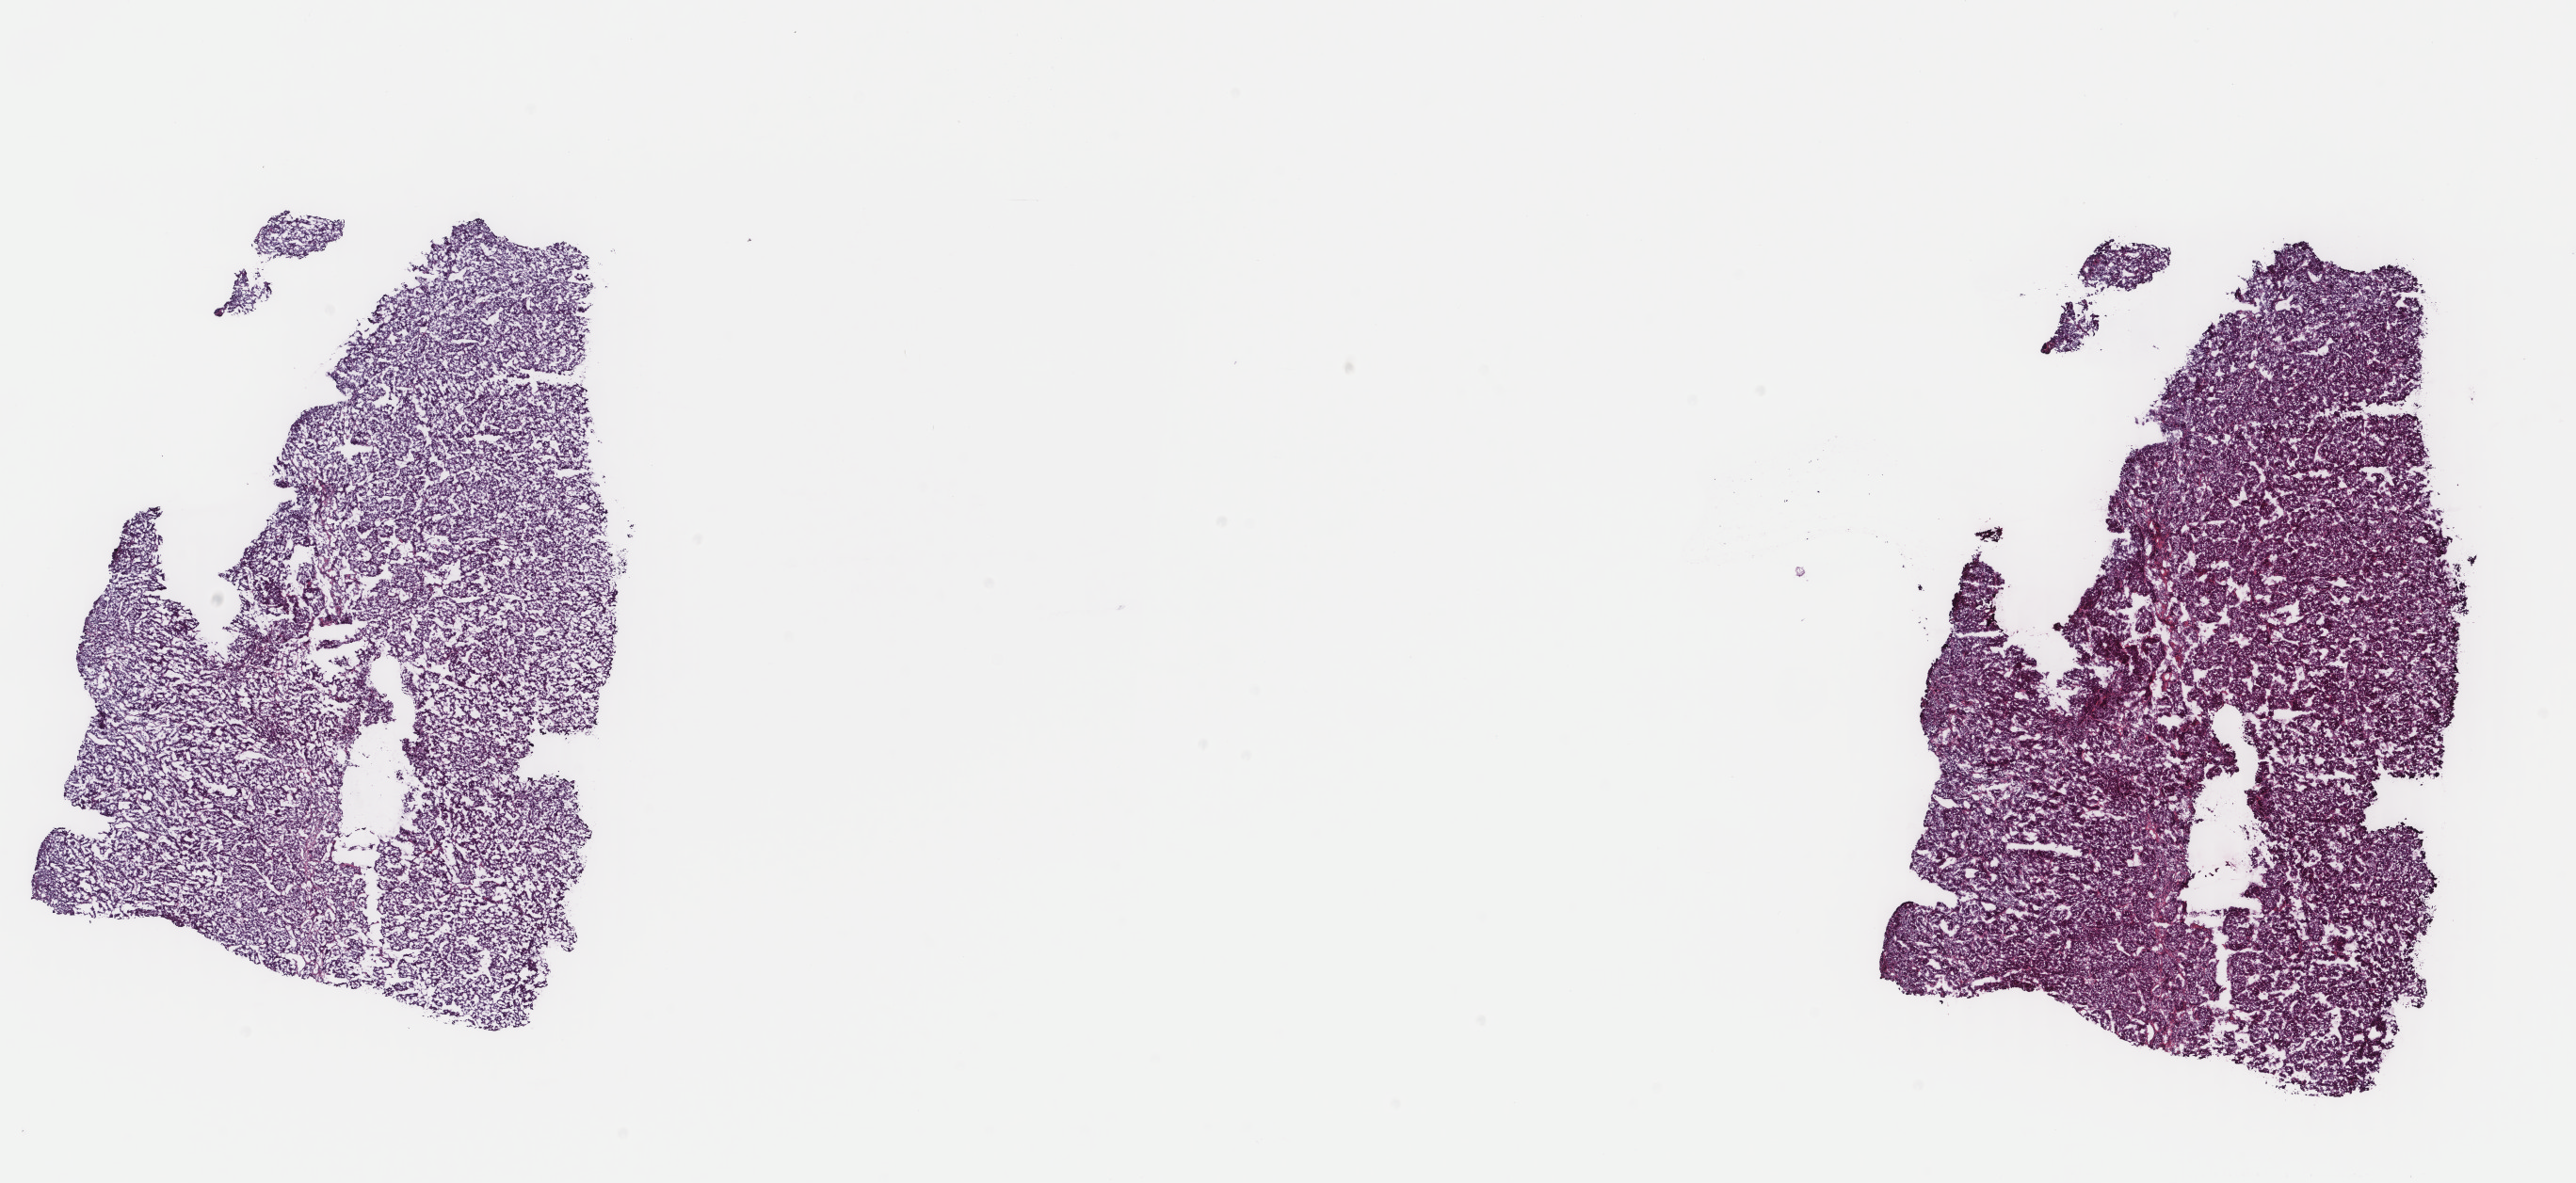
H&E-stained whole-slide image — whole scanned area (about 21.7 x 10.0 mm, from a 40x scan) shown as a low-resolution overview. Frozen section from the top of the tissue portion. Liver, primary tumour sample. Female, age 79 years at initial diagnosis. Histologic grade: G2 (moderately differentiated). Pathologist review of this section (percent, as recorded): tumour cells 100%, tumour nuclei 93%, normal cells 0%, stromal cells 0%, necrosis 0%. Infiltration values recorded for this section: lymphocyte infiltration 0%, monocyte infiltration 0%, neutrophil infiltration 0%.
AJCC pathologic stage: IIIB (7th edition). TNM: T3b N0 M0. Histologic diagnosis: Hepatocellular carcinoma, NOS.